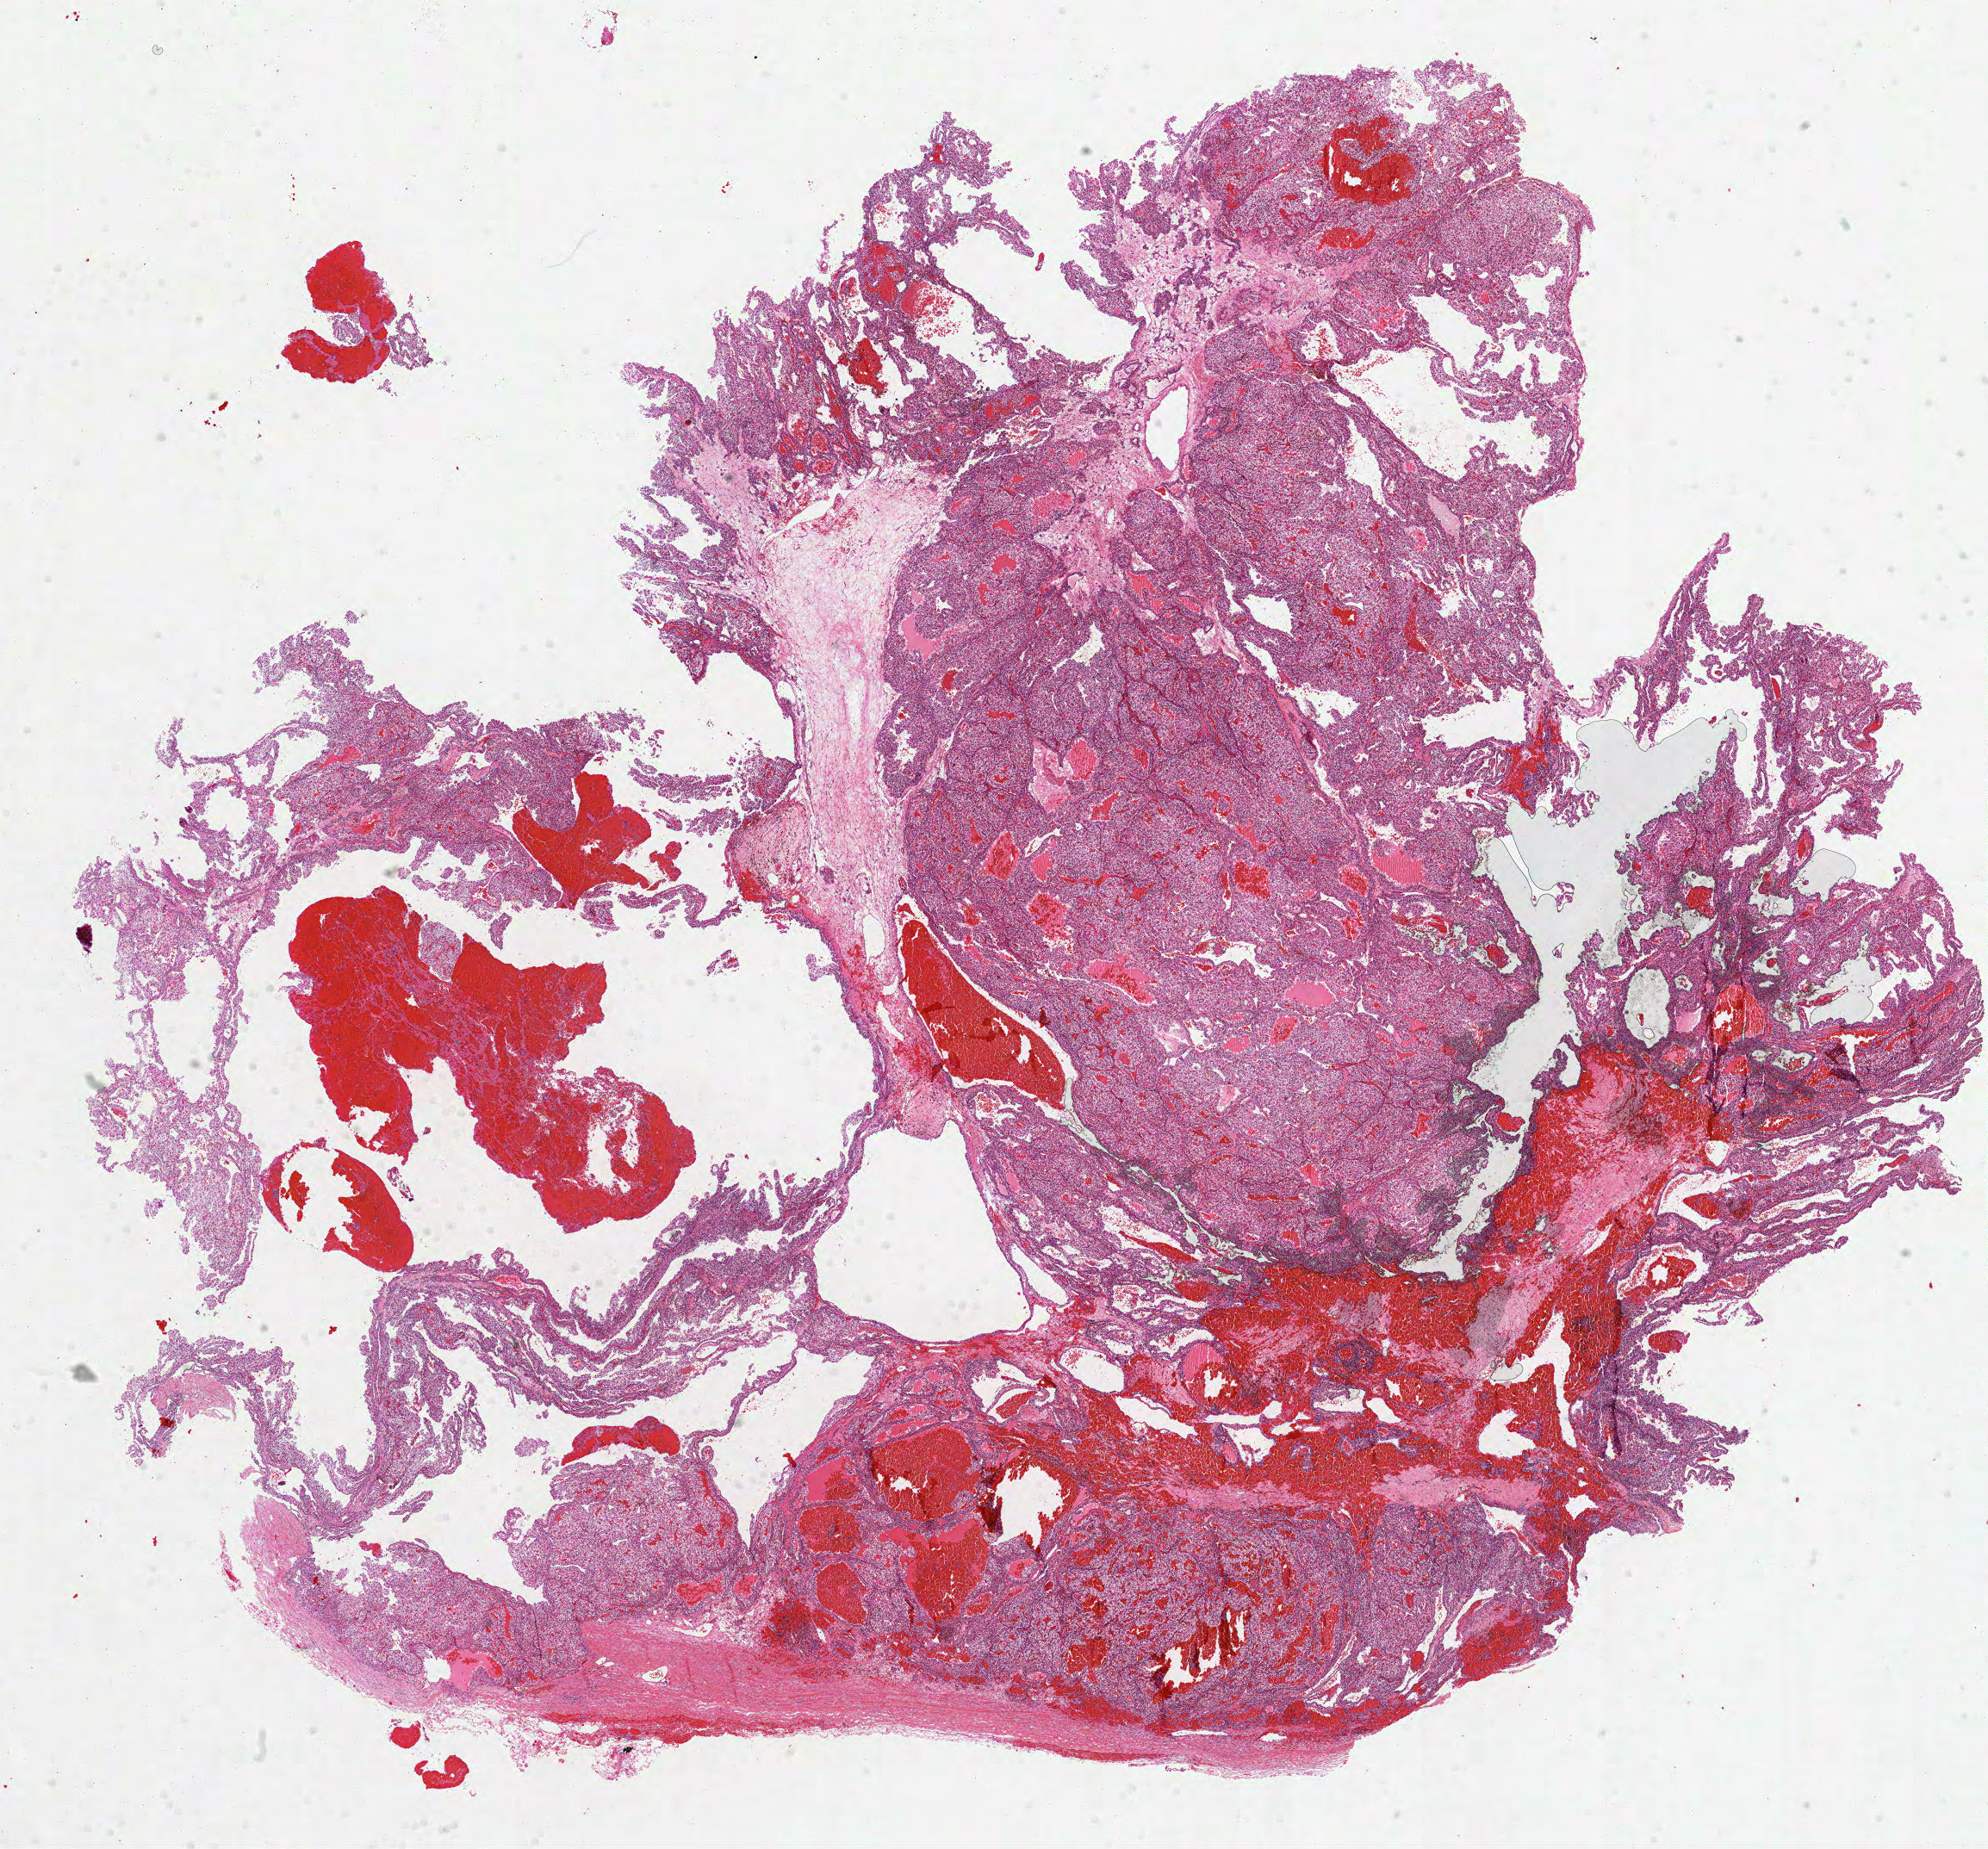
H&E whole-slide image — low-resolution overview of the scanned area, about 18.6 x 17.3 mm. Formalin-fixed paraffin-embedded (FFPE) diagnostic section. Kidney, primary tumour sample. Male, age 41 years at initial diagnosis. Histologic grade: G2 (moderately differentiated).
• diagnosis: Clear cell adenocarcinoma, NOS
• AJCC pathologic stage: I